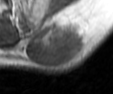
MRI of an extremity soft-tissue mass, one axial slice. Position 27 of 42 along the scan axis. MR volume resampled by the dataset authors to the PET/CT grid (not the native acquisition matrix). 3.27 mm slice thickness. 113 × 94 image matrix, field of view 110 × 92 mm. Male patient. From the clinical record (not read from this slice): histological type: leiomyosarcoma; grade: intermediate; site of the primary tumour: left pelvis.
Outlined on this slice (expert contour drawn on MRI and transferred to this co-registered scan by the dataset authors):
- gross tumour volume (mass): bounding box <26,20,89,69> (left, top, right, bottom; pixels)